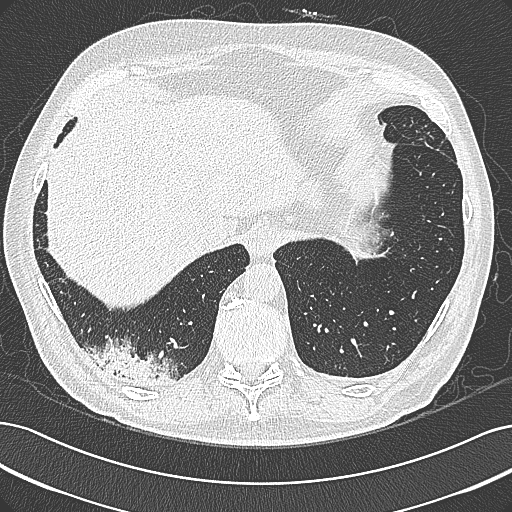
Low-dose screening chest CT, axial slice, first (baseline) screen, lung window (W 1500 / L -600 HU). Male, age 68 years at enrolment. Former smoker at enrolment.
- Expert reader's lesion annotation, box from (x=96, y=339) to (x=189, y=400) px.
- Screening reader's record for this exam: no non-calcified nodule ≥4 mm recorded.
- Lung cancer was diagnosed 154 days after this screen: mucinous adenocarcinoma, right lower lobe, well differentiated (G1), stage IB (AJCC 6th edition), 50 mm at pathology.